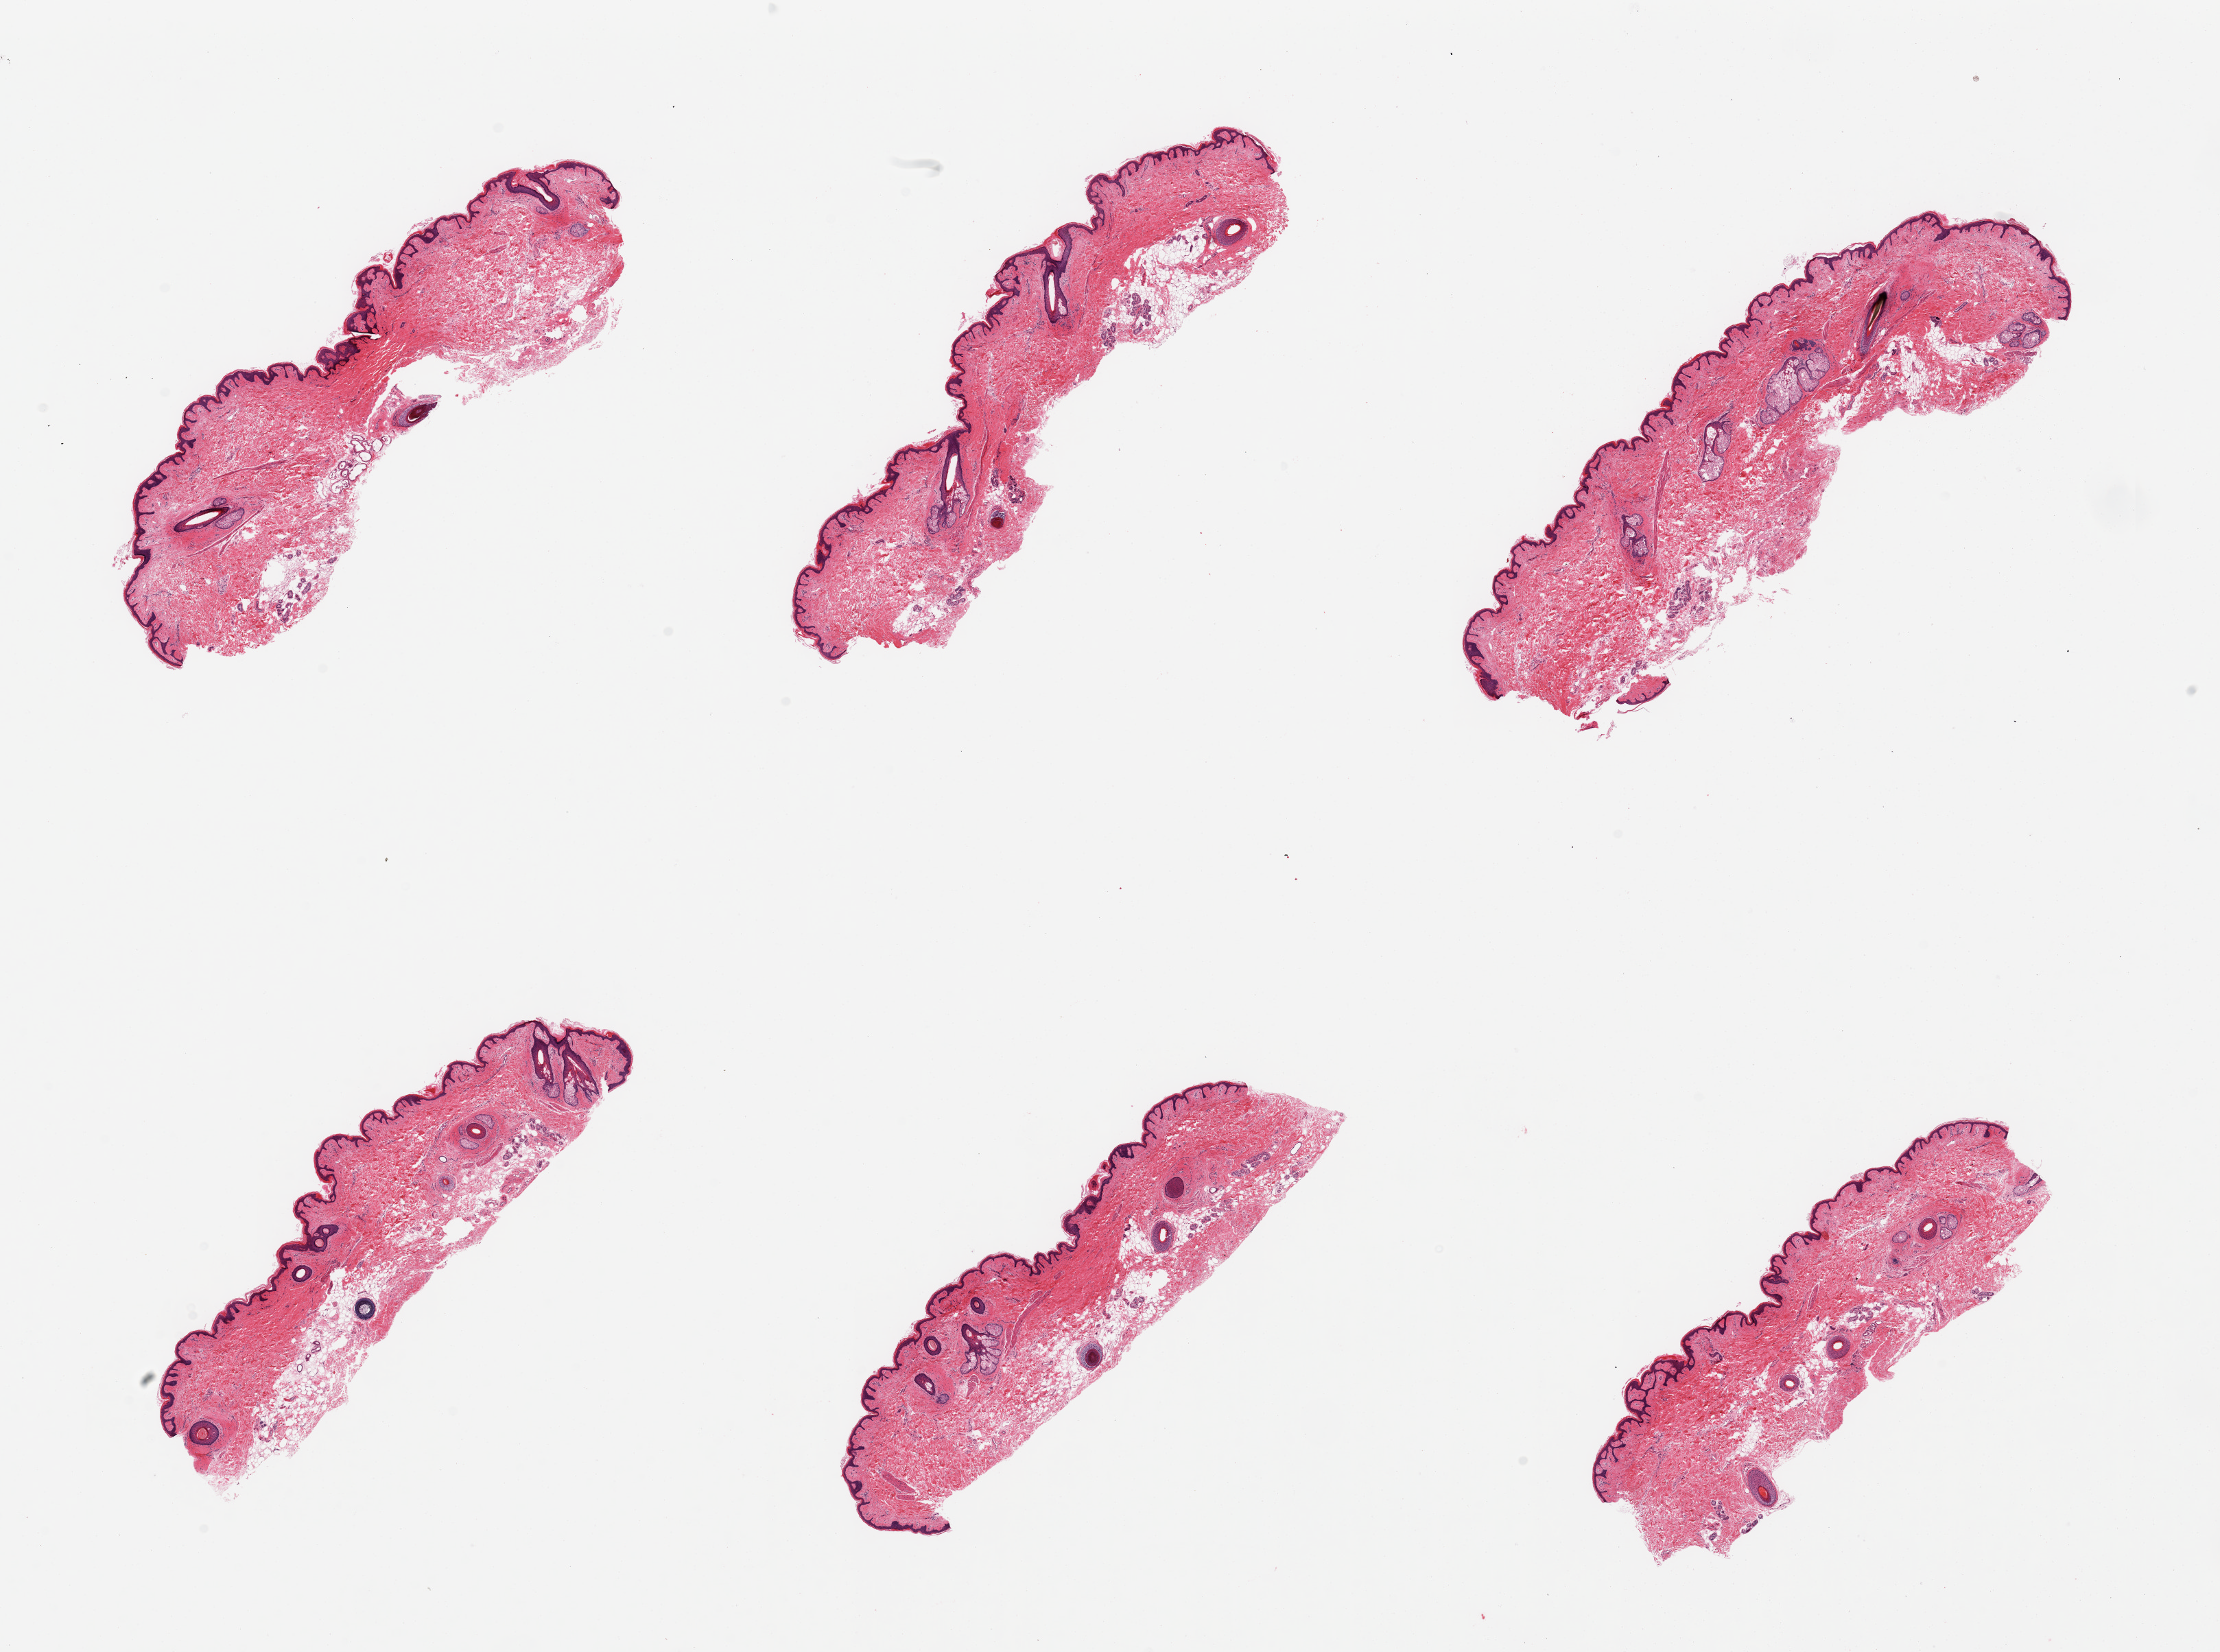
Whole-slide image, H&E stain — shown as a low-resolution overview of the whole scanned area (about 25.6 x 19.0 mm). PAXgene-fixed paraffin-embedded (PFPE) section. Section of skin of suprapubic region (target tissue). Donor tissue sample. Female donor.
Pathologist's review note for this sample: 6 pieces, minimal dermal fat; squamous epithelium is ~30 microns.